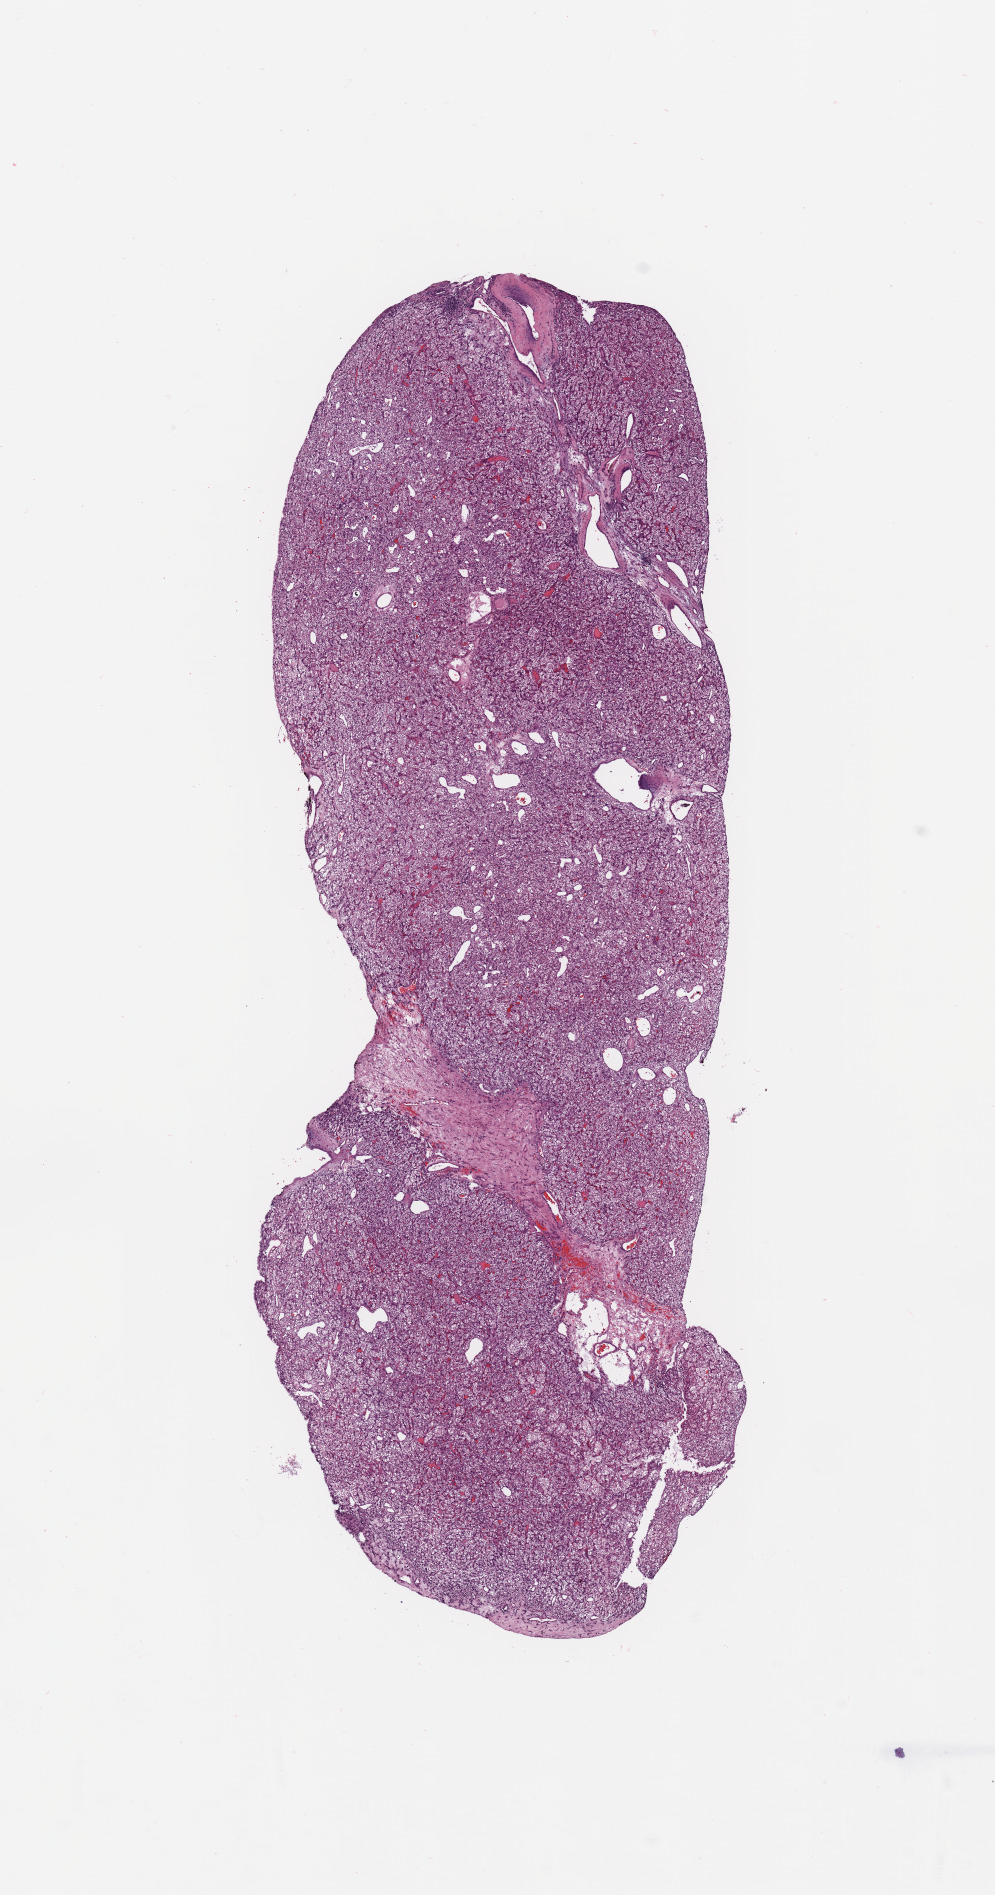
H&E-stained whole-slide image — whole scanned area (about 7.9 x 15.0 mm) shown as a low-resolution overview; tumour tissue sample, sampled site: kidney. Patient: female, age 76 years. Histologic grade: G2 (moderately differentiated). Slide review estimates, as recorded: tumour nuclei 90%, necrosis 0%.
AJCC pathologic stage: I. Diagnosis: Renal cell carcinoma, NOS. Primary tumour site (as recorded): middle.